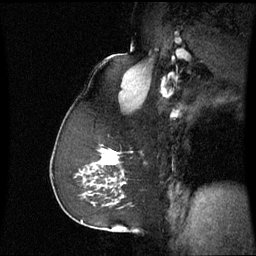
Breast MRI (dynamic contrast-enhanced), one sagittal slice; position 40 of 60 along the scan axis; dynamic contrast-enhanced series, image 2 of 3 at this slice position (ordered by acquisition); 1.5 T; TE 4.2 ms, TR 8.9 ms; 256 × 256 image matrix, field of view 220 × 220 mm. Patient: female, 59 years. Case-level facts recorded for this patient, not image findings: setting: breast cancer imaged before/during neoadjuvant chemotherapy; receptor status: triple-negative.
Annotated regions visible in this slice (semi-automatically segmented with operator editing):
- analysis volume of interest (the breast-tissue region the enhancement analysis was run in; not a lesion): bounding box (x1, y1, x2, y2) in pixels: (88, 146, 133, 197)
- tumour enhancement mask (voxels above the 70 % enhancement threshold inside the analysis volume of interest): (102, 152, 119, 165)